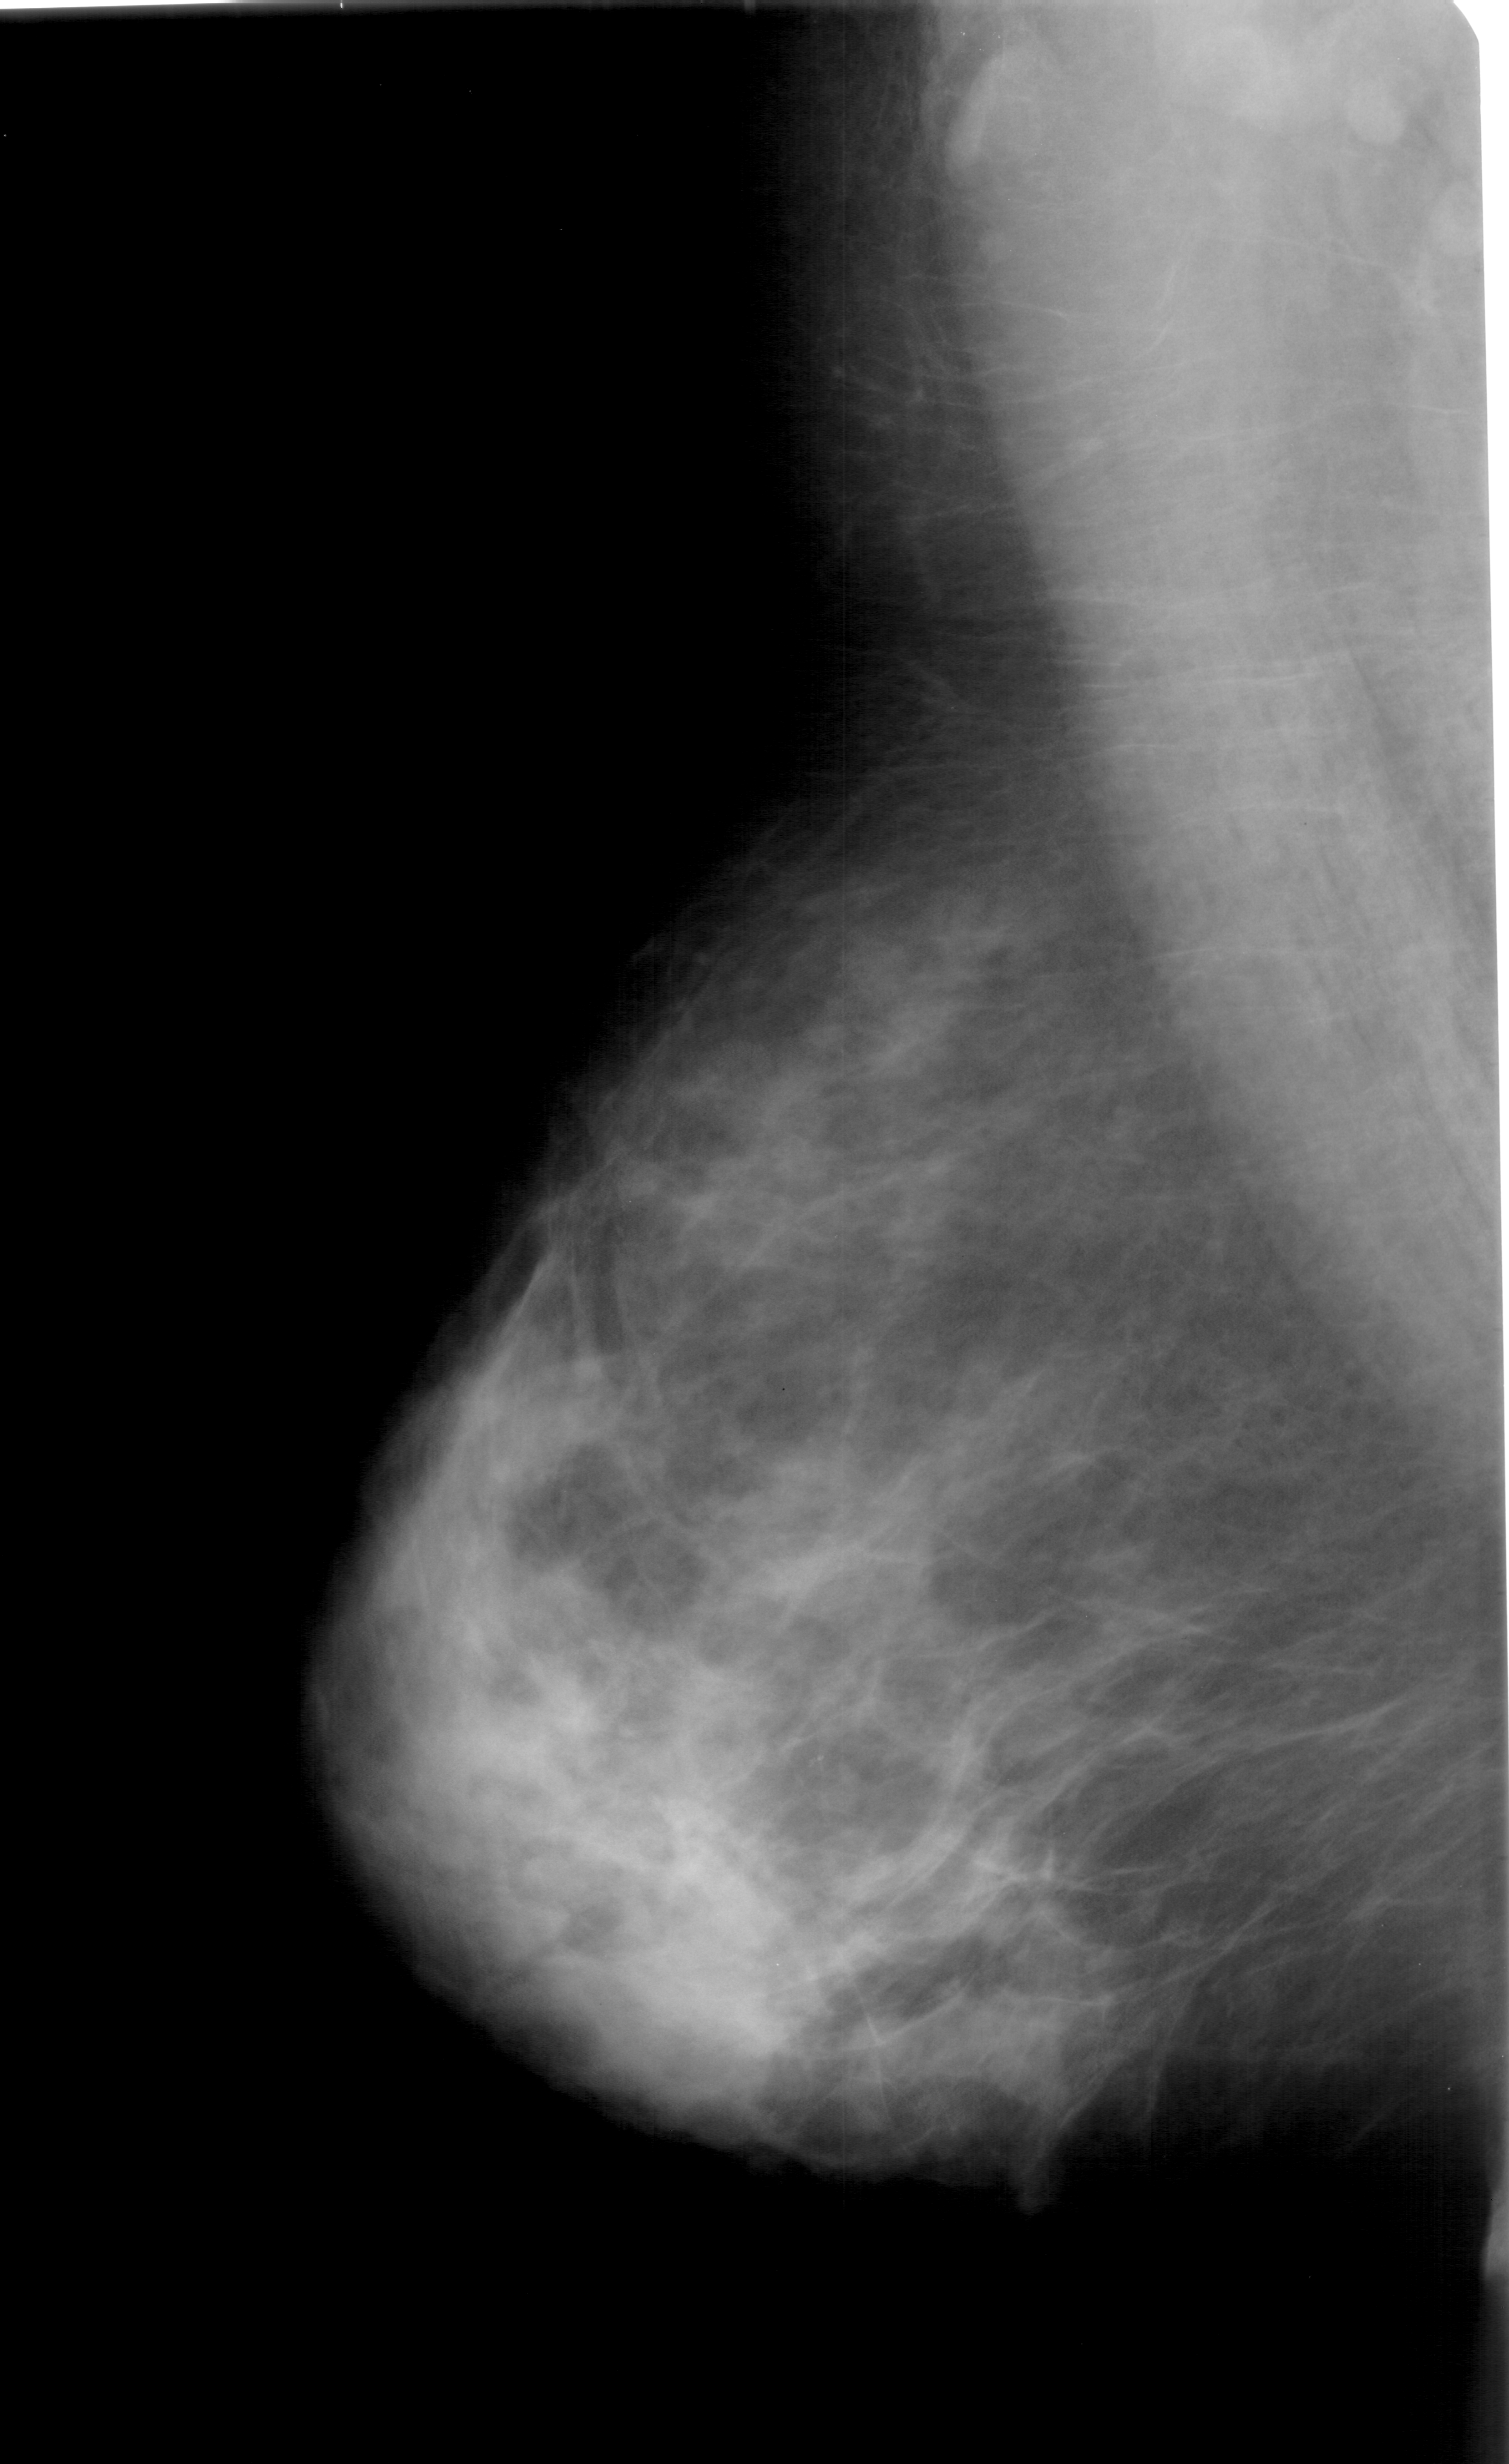
Scanned film-screen mammogram, left breast, mediolateral oblique (MLO) view, BI-RADS breast density category 4 (scale 1–4).
Calcifications, morphology pleomorphic, distribution clustered; BI-RADS assessment category 4; pathology result (as recorded, not read from the image): benign.